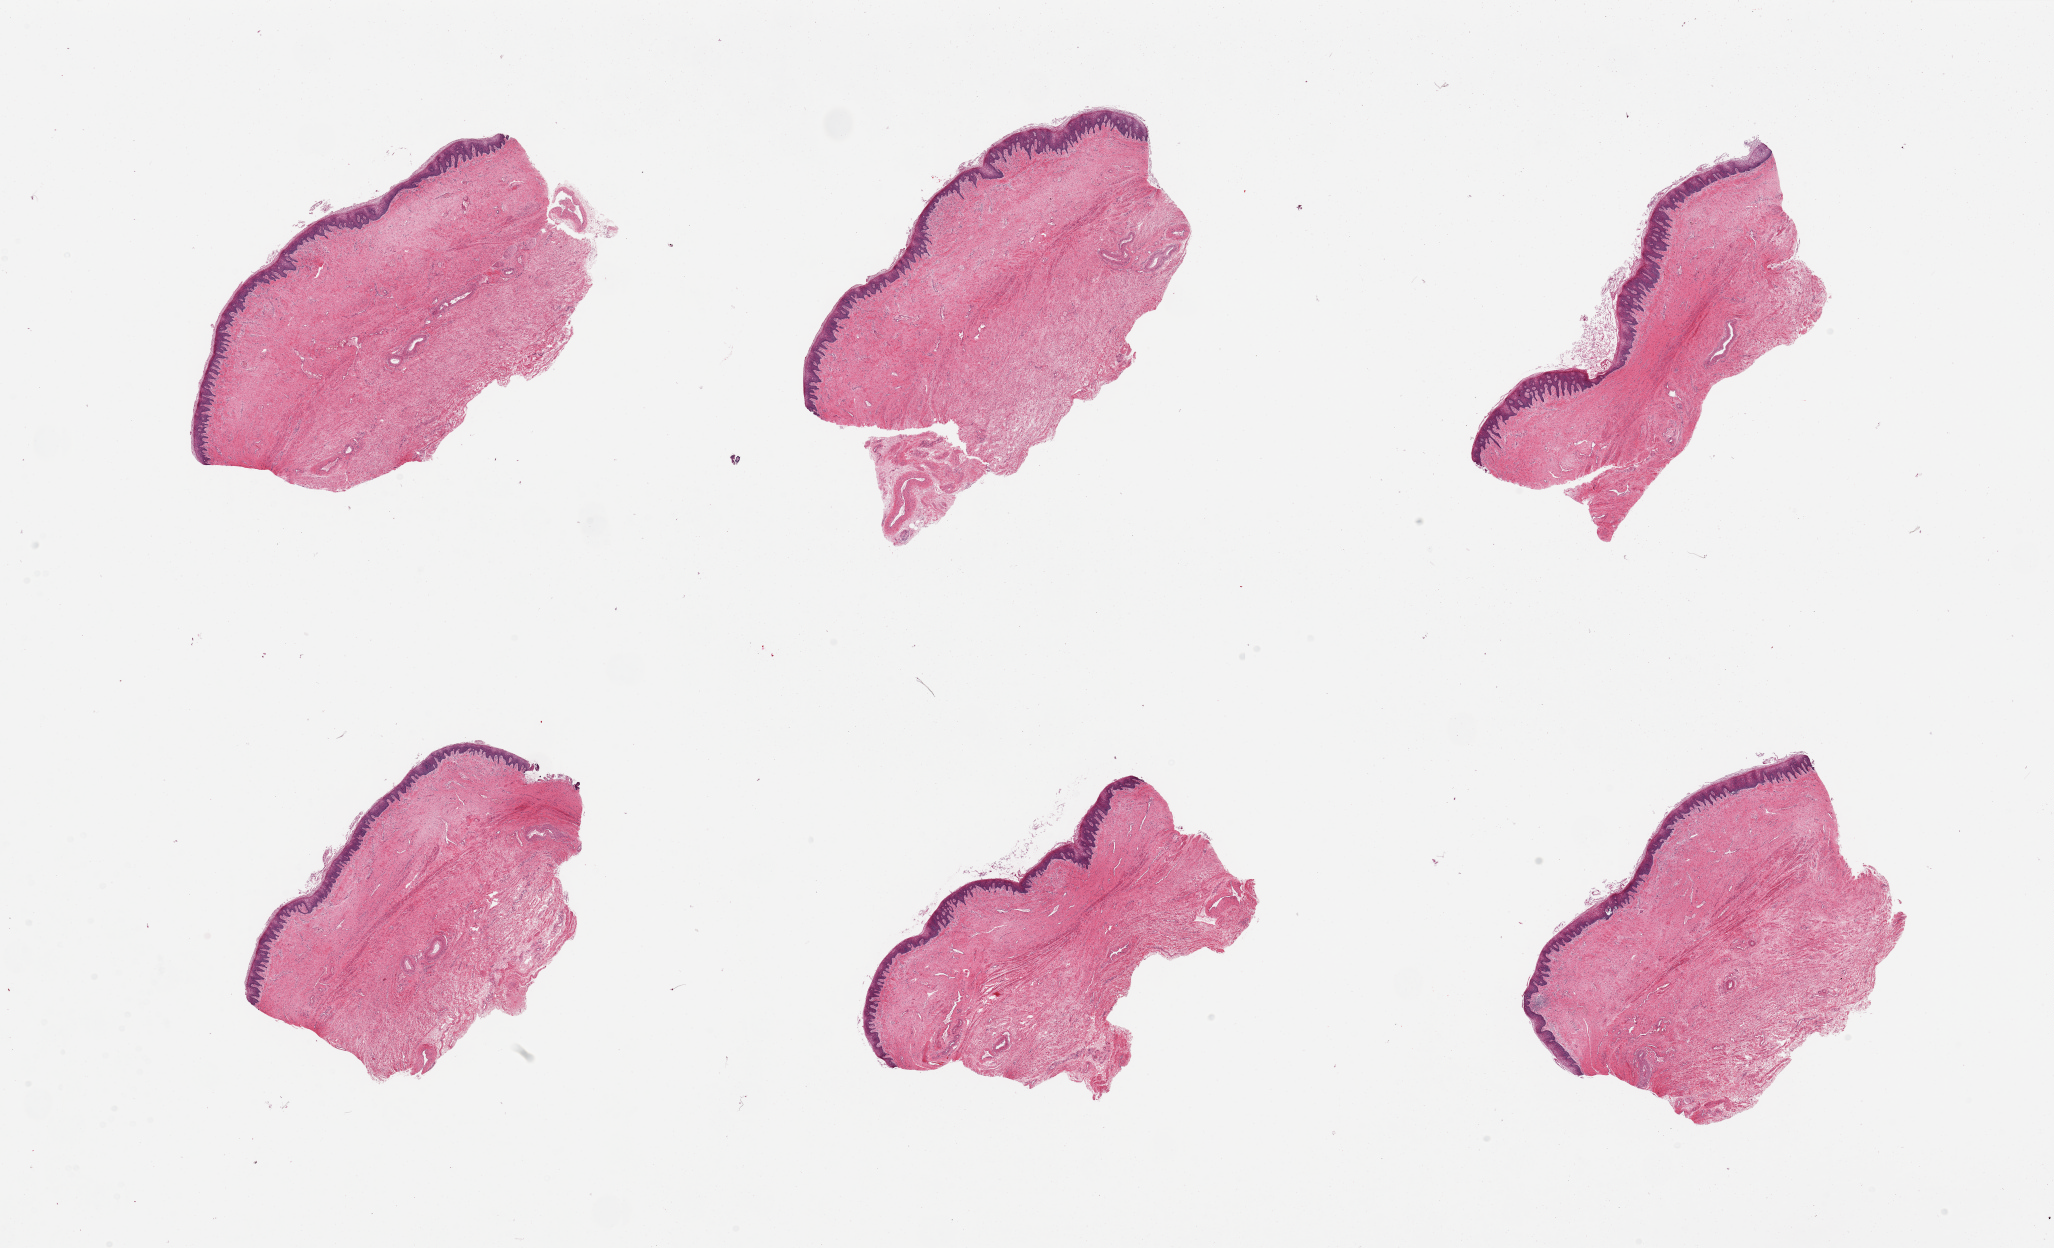
Hematoxylin and eosin (H&E) whole-slide image, brightfield, a low-resolution overview of the entire scanned area, about 32.5 x 19.7 mm, PAXgene-fixed, paraffin-embedded tissue, target tissue: vagina, donor tissue sample. Female donor.
Review note (as recorded): 6 pieces, squamous mucosa is ~5-6% thickness.